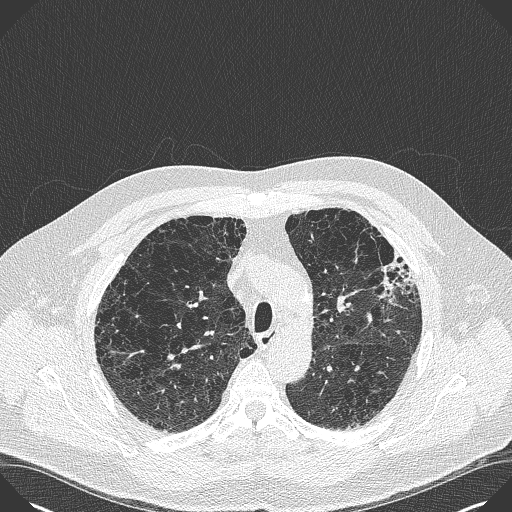
Chest CT (low-dose screening protocol), one axial image, first (baseline) screen, lung window (W 1500 / L -600 HU), 1 mm slice thickness, 120 kVp. Male, age 59 years at enrolment. Current smoker at enrolment.
• Expert-annotated lung lesion, bounding box [x1, y1, x2, y2] px = [373, 248, 428, 299].
• No non-calcified nodule or mass ≥4 mm was recorded by the screening reader at this exam.
• Official screen result: negative screen, minor abnormalities not suspicious for lung cancer.
• Lung cancer was diagnosed 909 days after this screen (after the third annual screen): bronchiolo-alveolar carcinoma, mixed mucinous and non-mucinous, left upper lobe, stage IA (AJCC 6th edition), 20 mm at pathology.